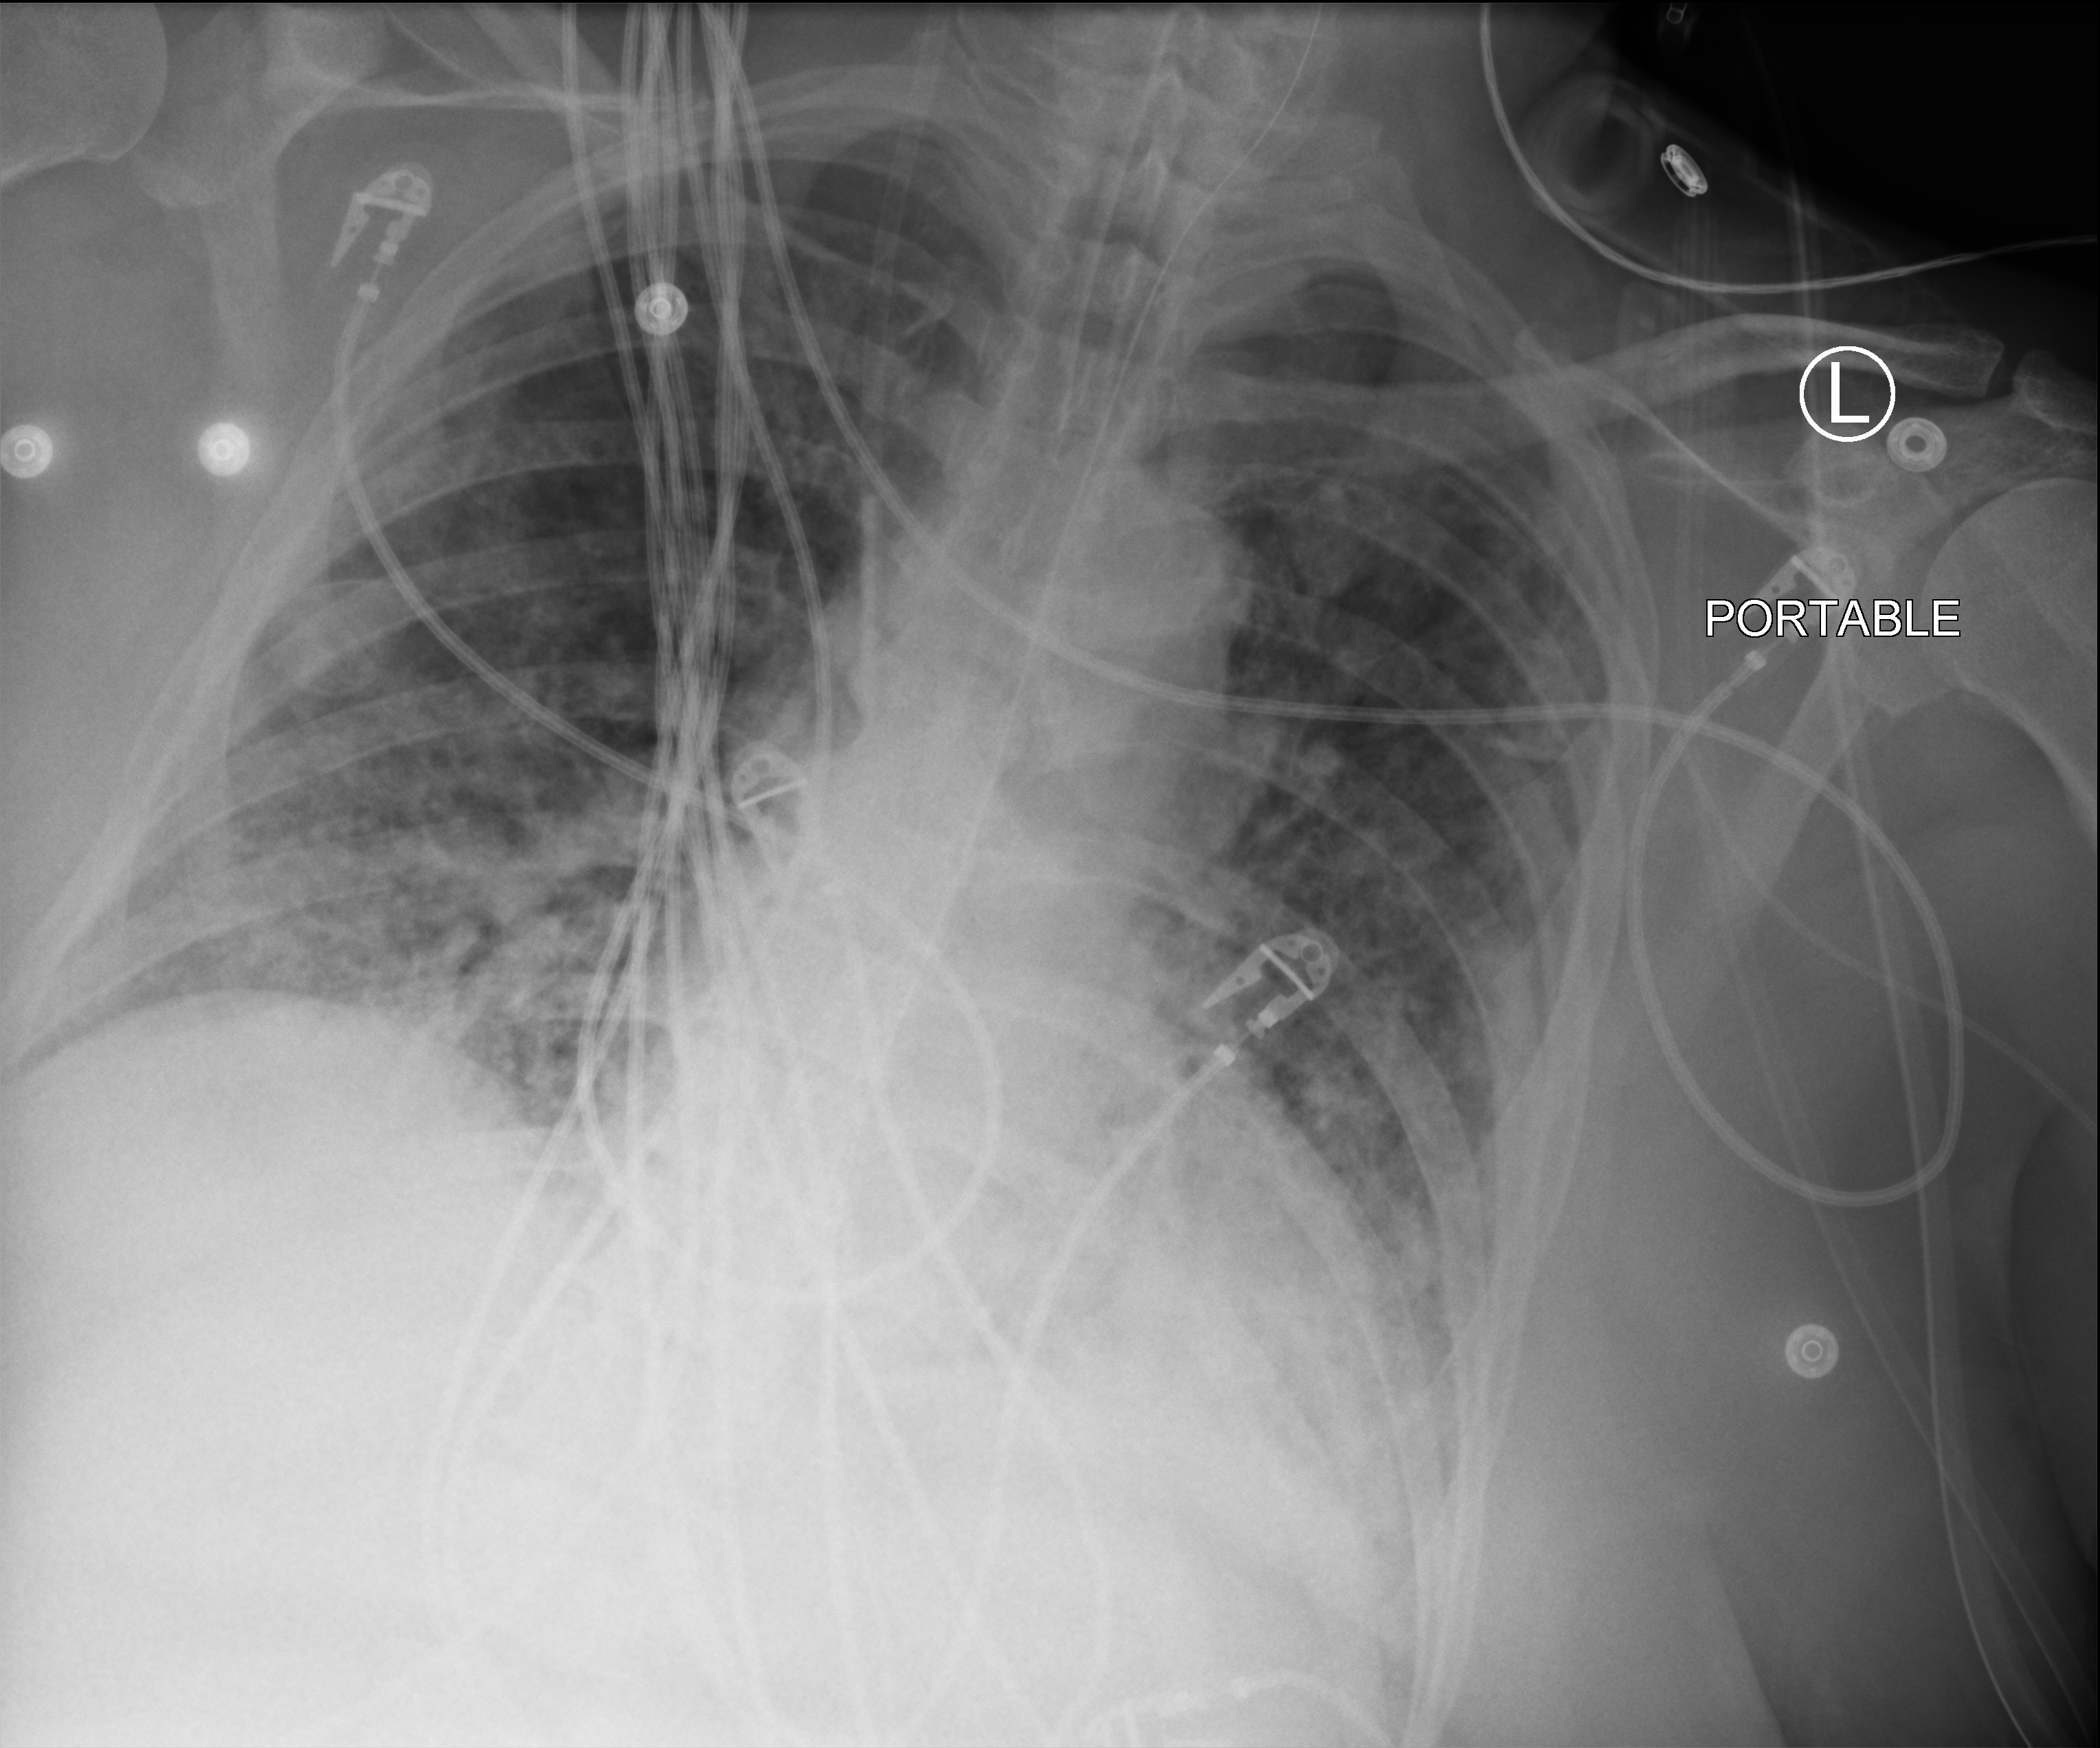
Chest X-ray (portable); anteroposterior (AP) projection. Patient hospitalised with COVID-19; male, aged 60–74 years.
Hospital-stay facts (about this admission, not read from this image; timing relative to this image not recorded): mechanically ventilated during this hospital stay: yes; admitted to intensive care during this hospital stay: yes.